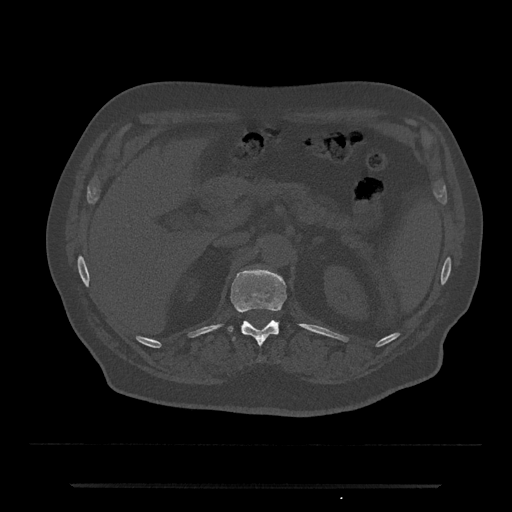
CT including the spine, one axial slice; slice 587 of 797 in the series (ordered by position); 120 kVp; bone window (W 1800 / L 400 HU); 0.5 mm slice thickness; 512 × 512 image matrix, field of view 434 × 434 mm. Patient: male, 80 years. Case-level facts recorded for this patient, not image findings: primary cancer: prostate; vertebrae with lytic lesions (as recorded): L1, T11.
Outlined on this slice (semi-automatically segmented with operator editing):
- T12 vertebra: bounding box [x1, y1, x2, y2] px = [229, 269, 287, 361]